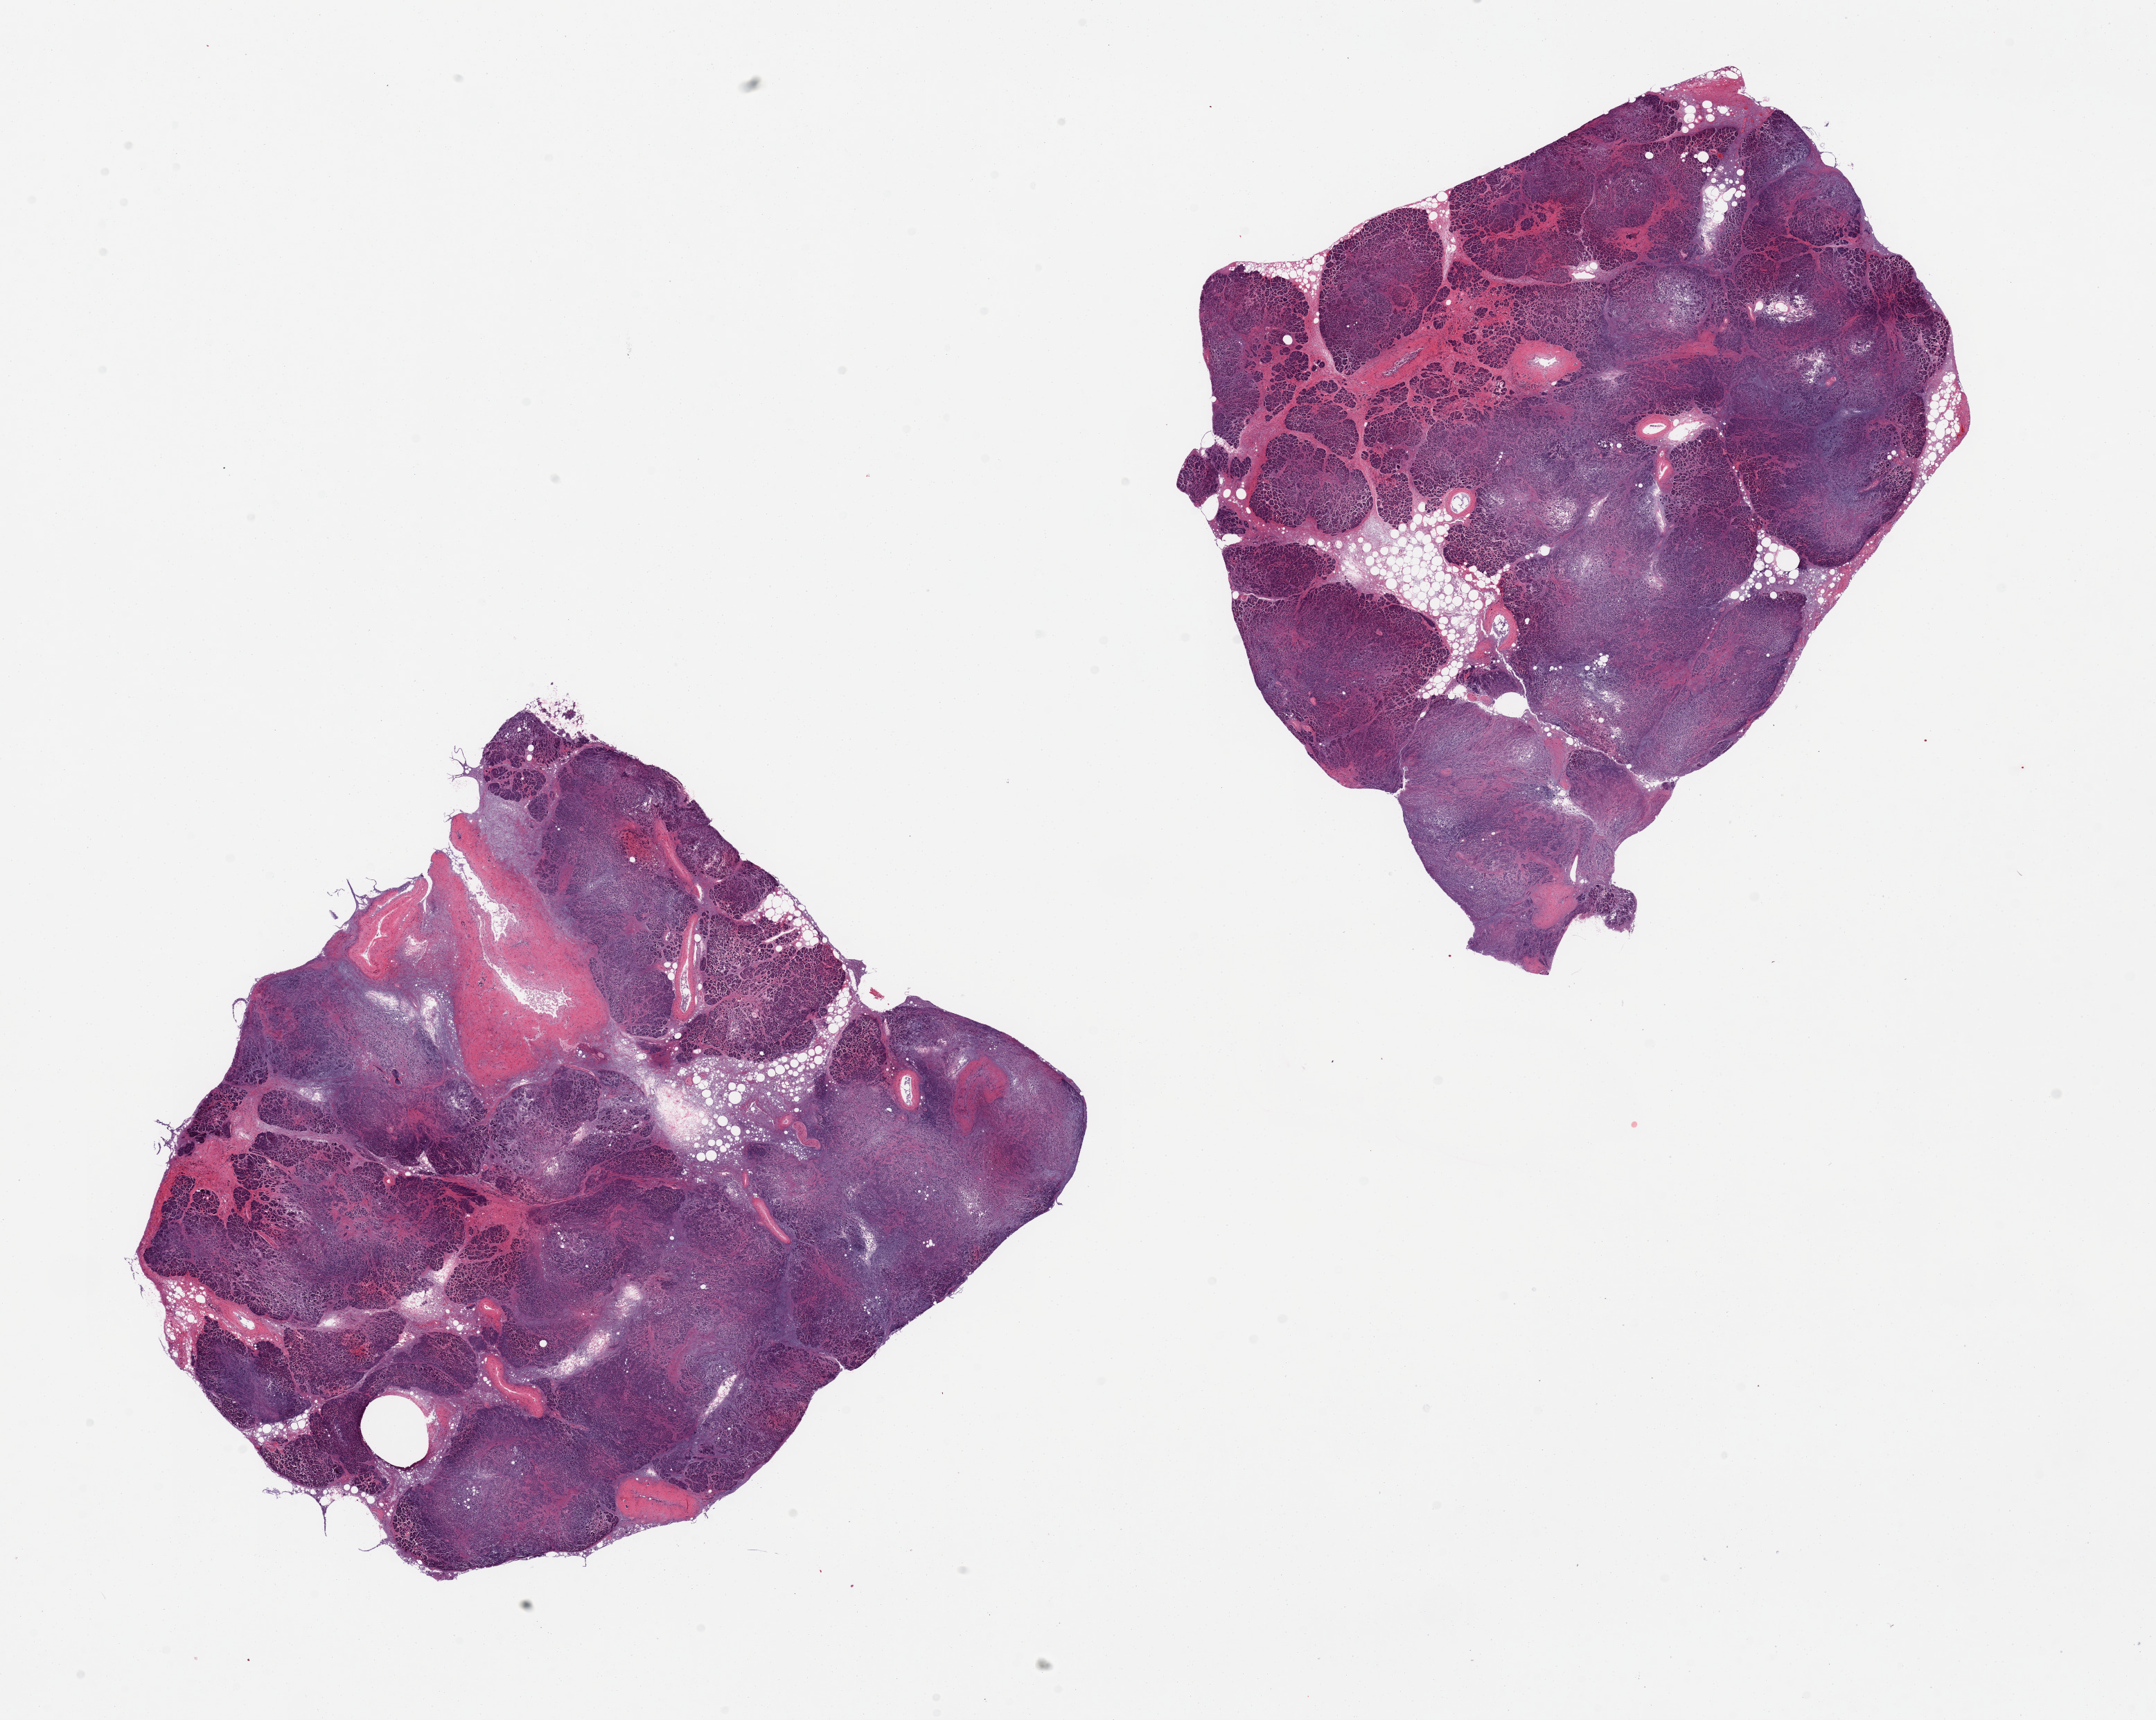
H&E whole-slide image, a low-resolution overview of the entire scanned area, about 24.6 x 19.6 mm (slide scanned at 20x). PAXgene-fixed, paraffin-embedded tissue. Section of pancreas (target tissue). Donor tissue sample. Donor sex: male.
Review note (as recorded): 2 pieces, marked saponification/autolysis; Islets not visualized.